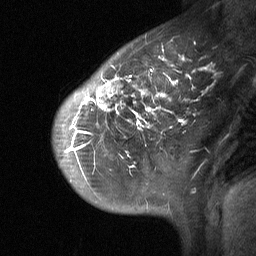
Breast MRI (dynamic contrast-enhanced), one sagittal slice; slice 45 of 64 in the series (ordered by position); dynamic contrast-enhanced study with each time point stored as its own series, time point 2 of 3 at this slice position (early post-contrast, ordered by acquisition time); 1.5 T; TE 4.8 ms, TR 27 ms; 256 × 256 image matrix, field of view 200 × 200 mm. Patient: female, 42 years. Case-level facts recorded for this patient, not image findings: setting: breast cancer imaged before/during neoadjuvant chemotherapy; receptor status: triple-negative.
Outlined on this slice (semi-automatically segmented with operator editing):
- analysis volume of interest (the breast-tissue region the enhancement analysis was run in; not a lesion): bounding box [x1, y1, x2, y2] px = [53, 29, 203, 190]
- tumour enhancement mask (voxels above the 90 % enhancement threshold inside the analysis volume of interest): [65, 75, 191, 153]